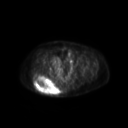
FDG PET of an extremity soft-tissue mass (from a PET/CT study), one axial slice. Slice 61 of 267 in the series (ordered by position). 3.27 mm slice thickness. 128 × 128 image matrix. Patient: female, 60 years. From the clinical record (not read from this slice): histological type: spindle cell suggestive of myxofibrosarcoma; grade: intermediate; site of the primary tumour: right buttock.
Structures marked on this image (expert contour drawn on MRI and transferred to this co-registered scan by the dataset authors):
- gross tumour volume (mass): bounding box <34,76,60,95> (left, top, right, bottom; pixels)